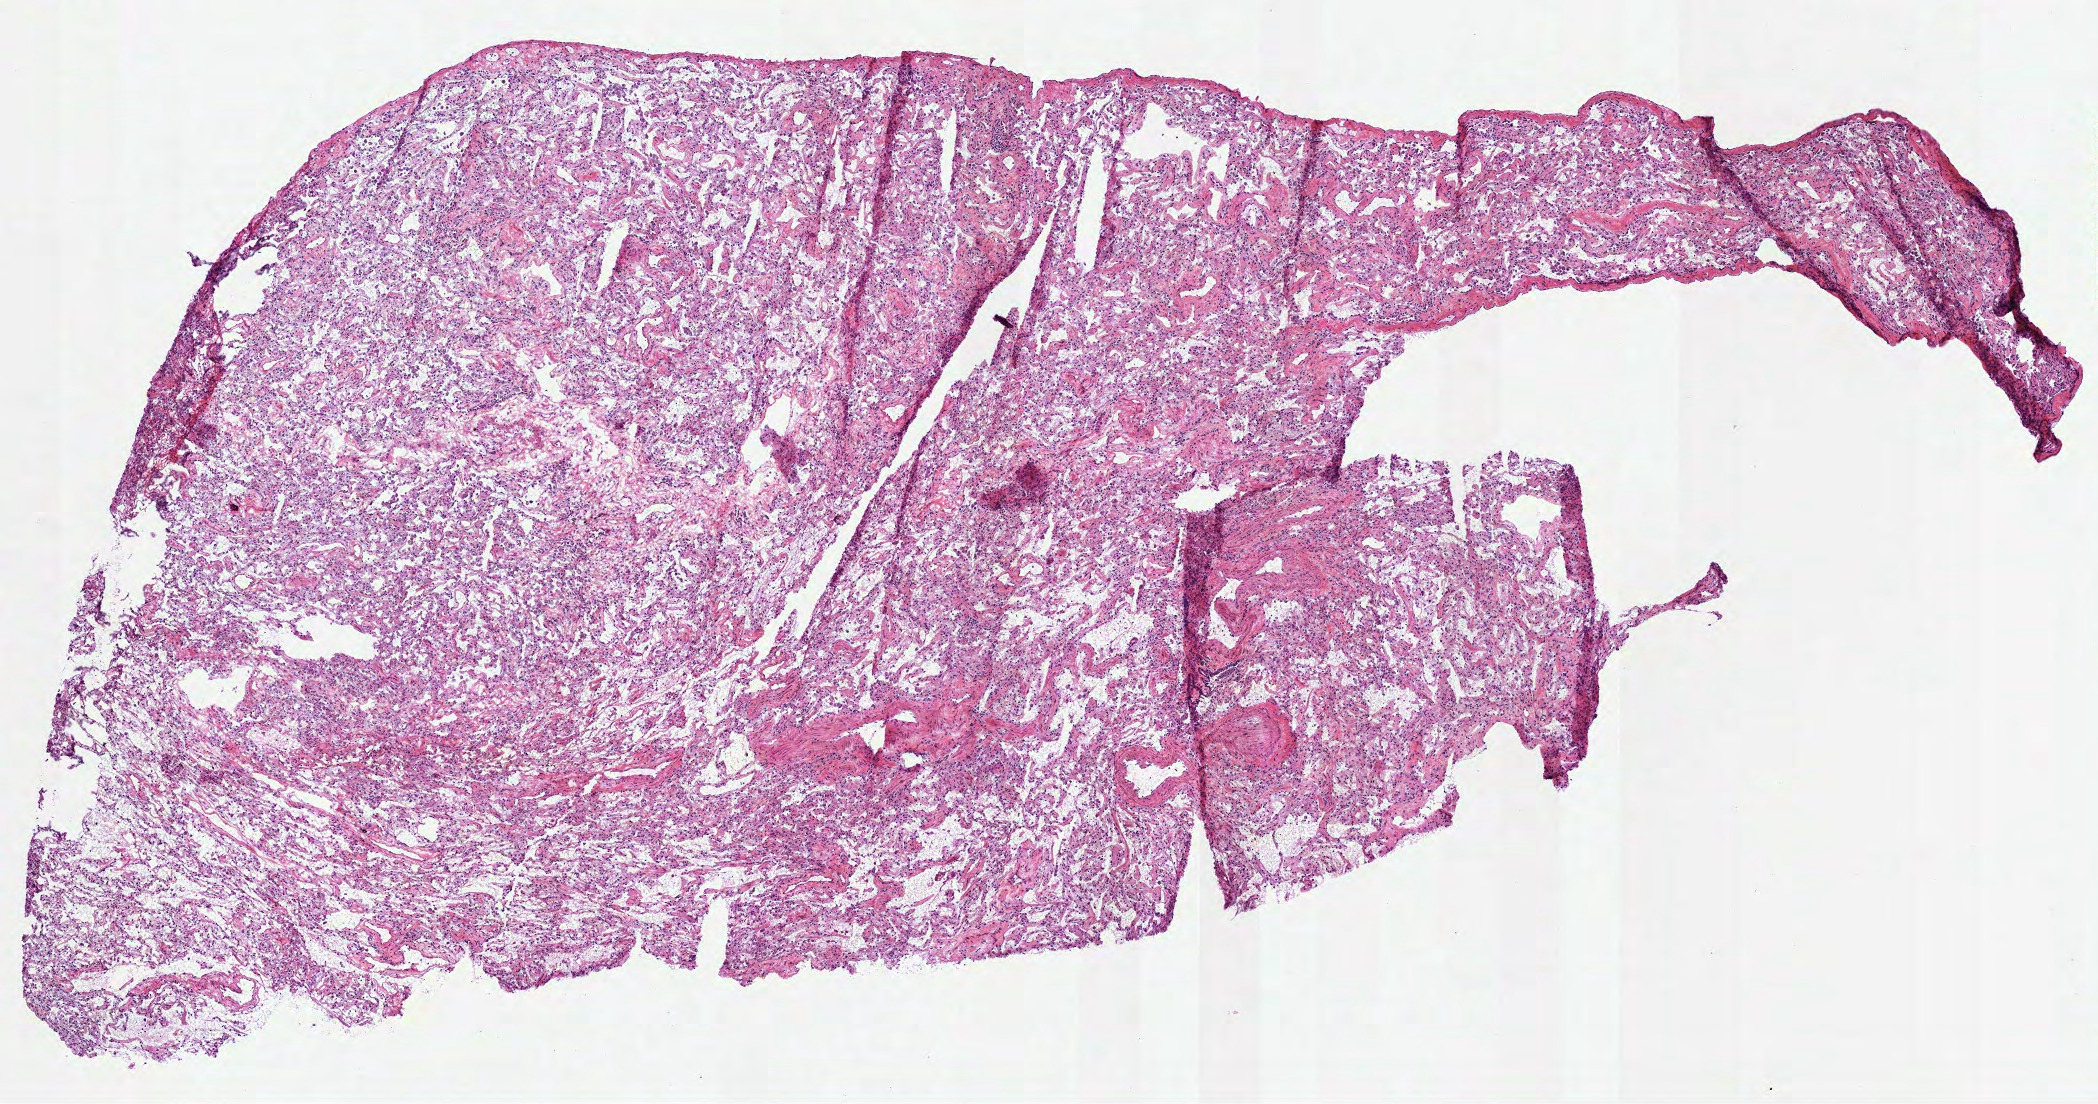
Digitized H&E-stained tissue section (whole slide), a low-resolution overview of the entire scanned area, about 8.5 x 4.5 mm (acquisition: 40x scan); frozen section from the top of the tissue portion; sample: solid tissue normal (non-tumour tissue), lung. Patient: female, age at initial diagnosis 63 years.
This section: solid tissue normal sample (biorepository sample class). Patient diagnosis: Bronchiolo-alveolar carcinoma, non-mucinous (lower lobe, lung).